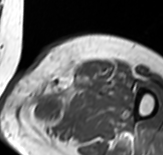
MRI of an extremity soft-tissue mass, one axial slice. Position 47 of 65 along the scan axis. MR volume resampled by the dataset authors to the PET/CT grid (not the native acquisition matrix). 3.27 mm slice thickness. 163 × 155 image matrix, field of view 159 × 151 mm. Female patient. Case-level facts recorded for this patient, not image findings: histological type: pleomorphic leiomyosarcoma; grade: high; site of the primary tumour: left thigh.
Structures marked on this image (expert contour drawn on MRI and transferred to this co-registered scan by the dataset authors):
- gross tumour volume including surrounding oedema: box from (x=26, y=63) to (x=97, y=134) px